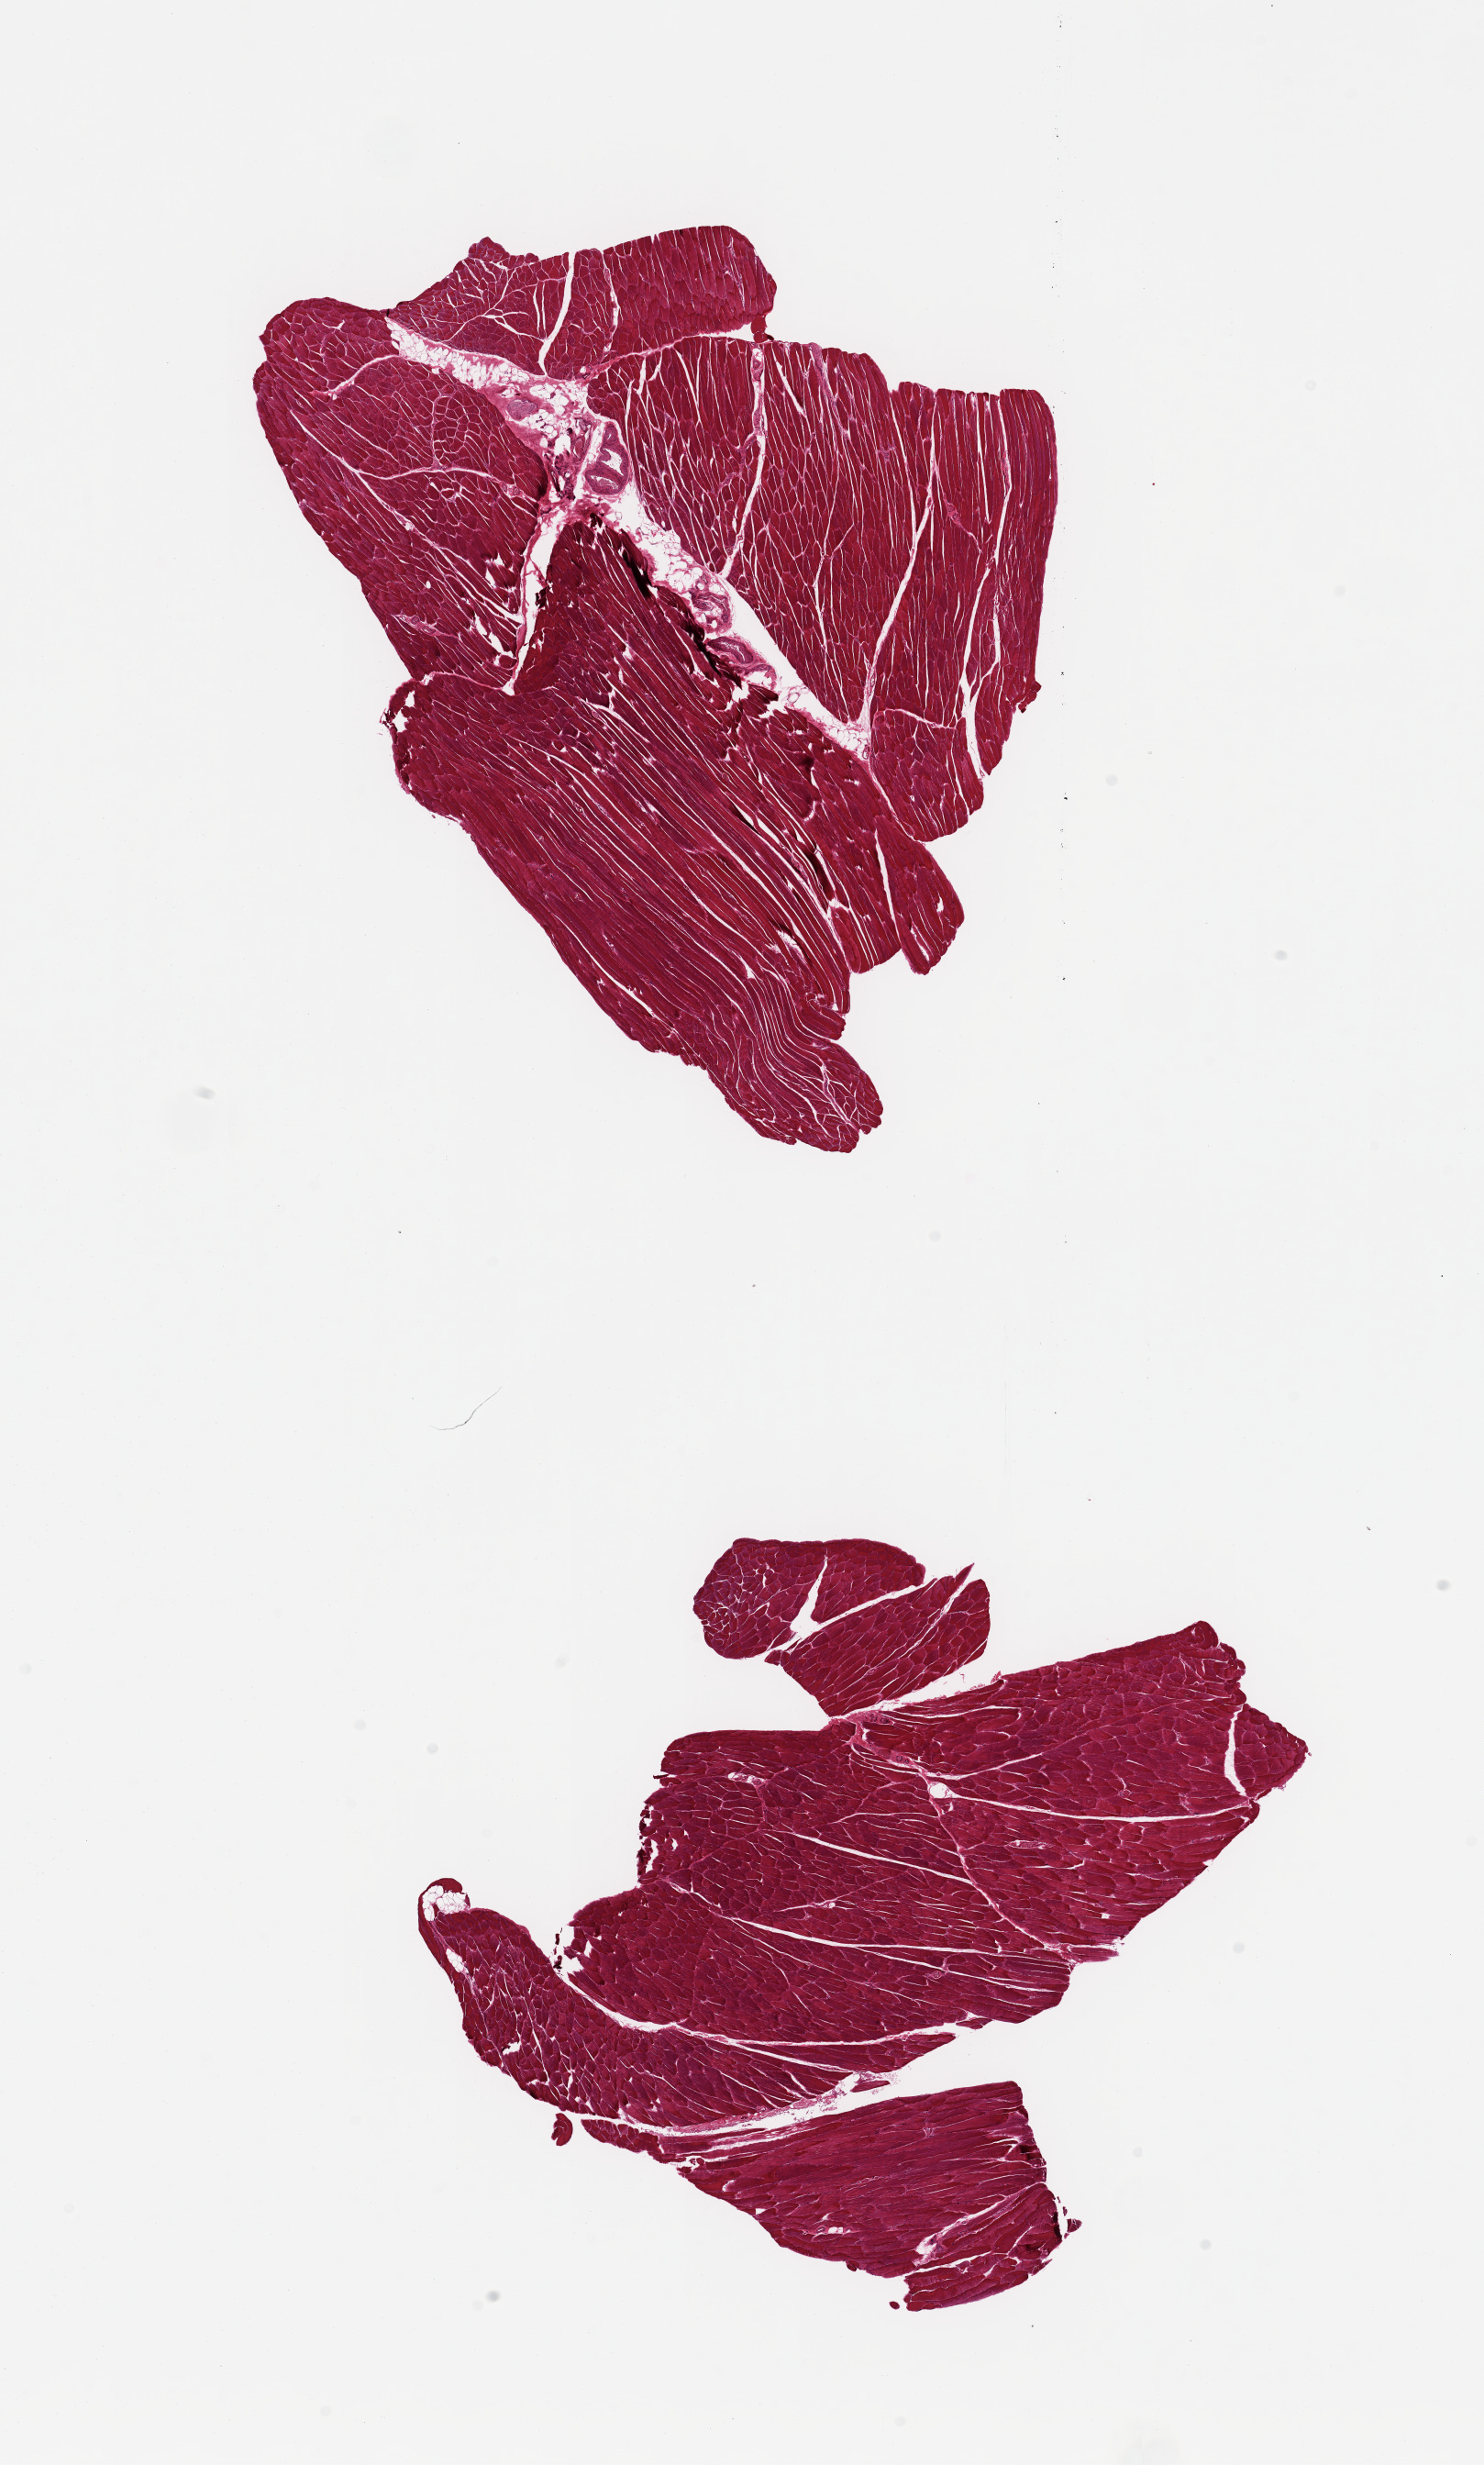
H&E whole-slide image, brightfield — whole scanned area (about 12.8 x 21.3 mm, acquisition: 20x scan) shown as a low-resolution overview. PAXgene-fixed, paraffin-embedded tissue. Sampled site (target tissue): skeletal muscle. Donor tissue sample. Donor: male.
Reviewer comment on this tissue sample: 2 pieces, 5-10% interstitial fat/vascular elements.